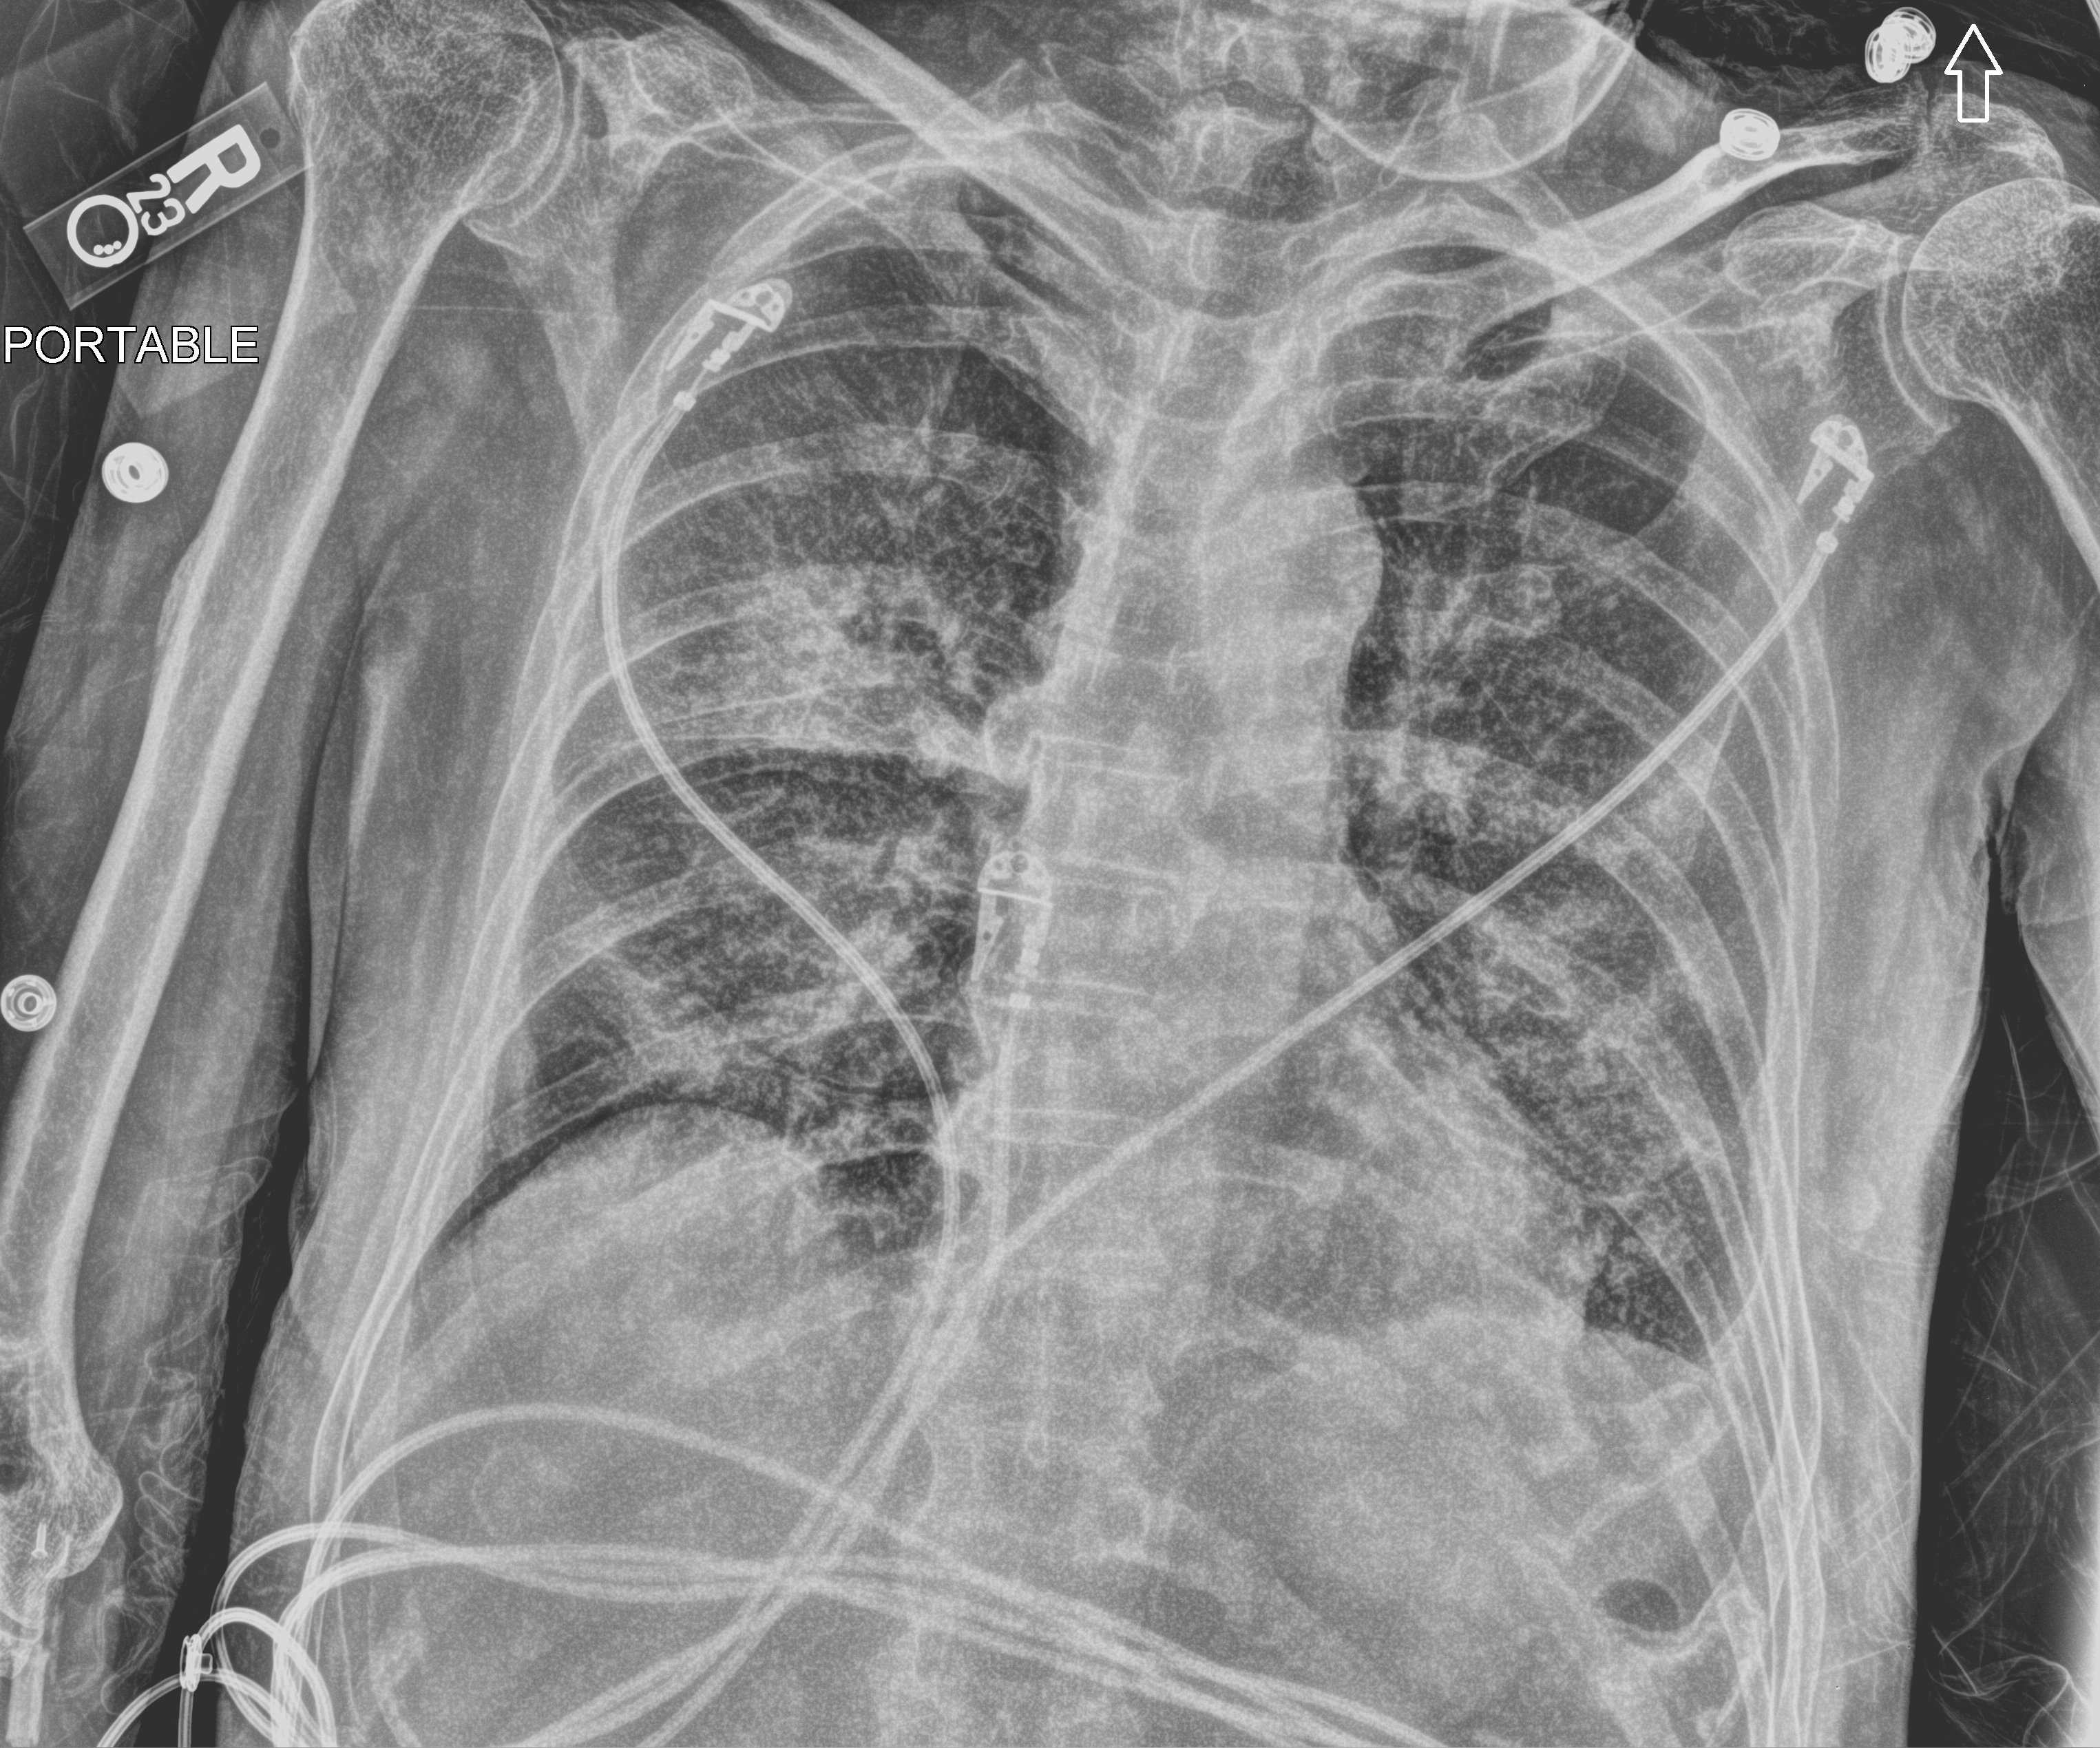
Chest X-ray (portable), anteroposterior (AP) projection. Male patient hospitalised with COVID-19, age 60–74 years.
From the hospital-stay record, not from the radiograph (when in the stay this image was taken is not recorded): mechanically ventilated during this hospital stay: yes.